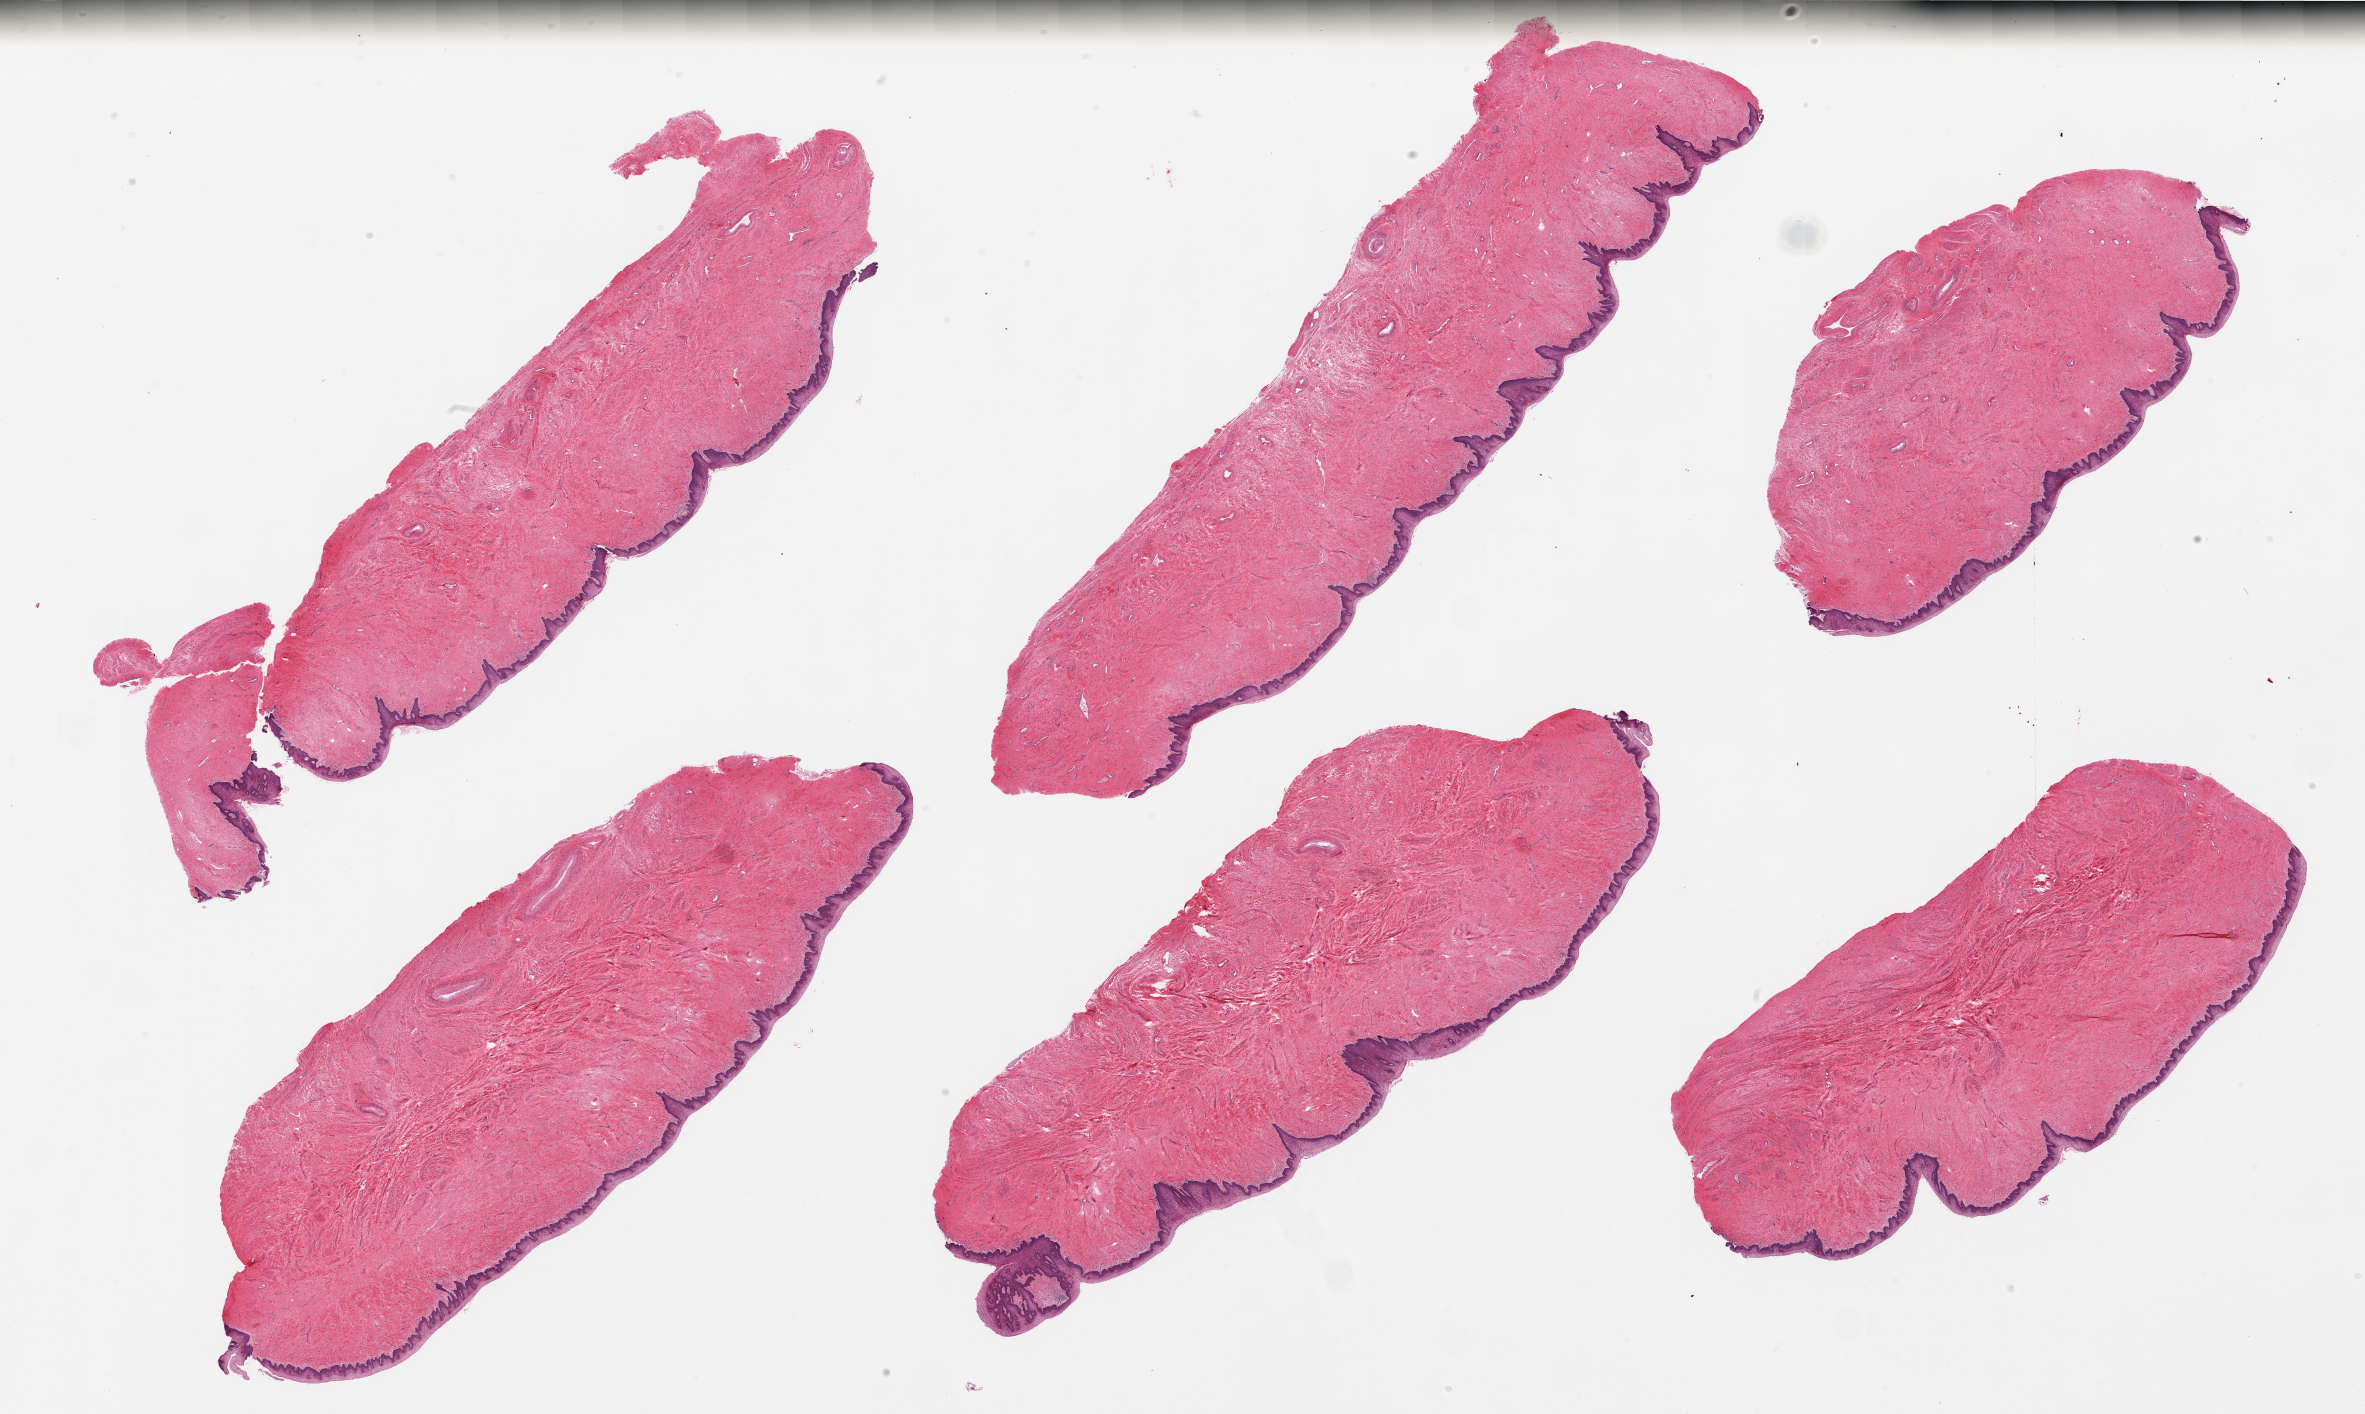
Whole-slide image, haematoxylin and eosin stain — low-resolution overview of the scanned area, about 37.4 x 22.4 mm (from a 20x scan), PAXgene-fixed, paraffin-embedded tissue, sampled site (target tissue): vagina, donor tissue sample. Female donor.
Pathologist's review note for this sample: 6 pieces; squamous mucosa is ~0.25mm thick, 10% total thickness.